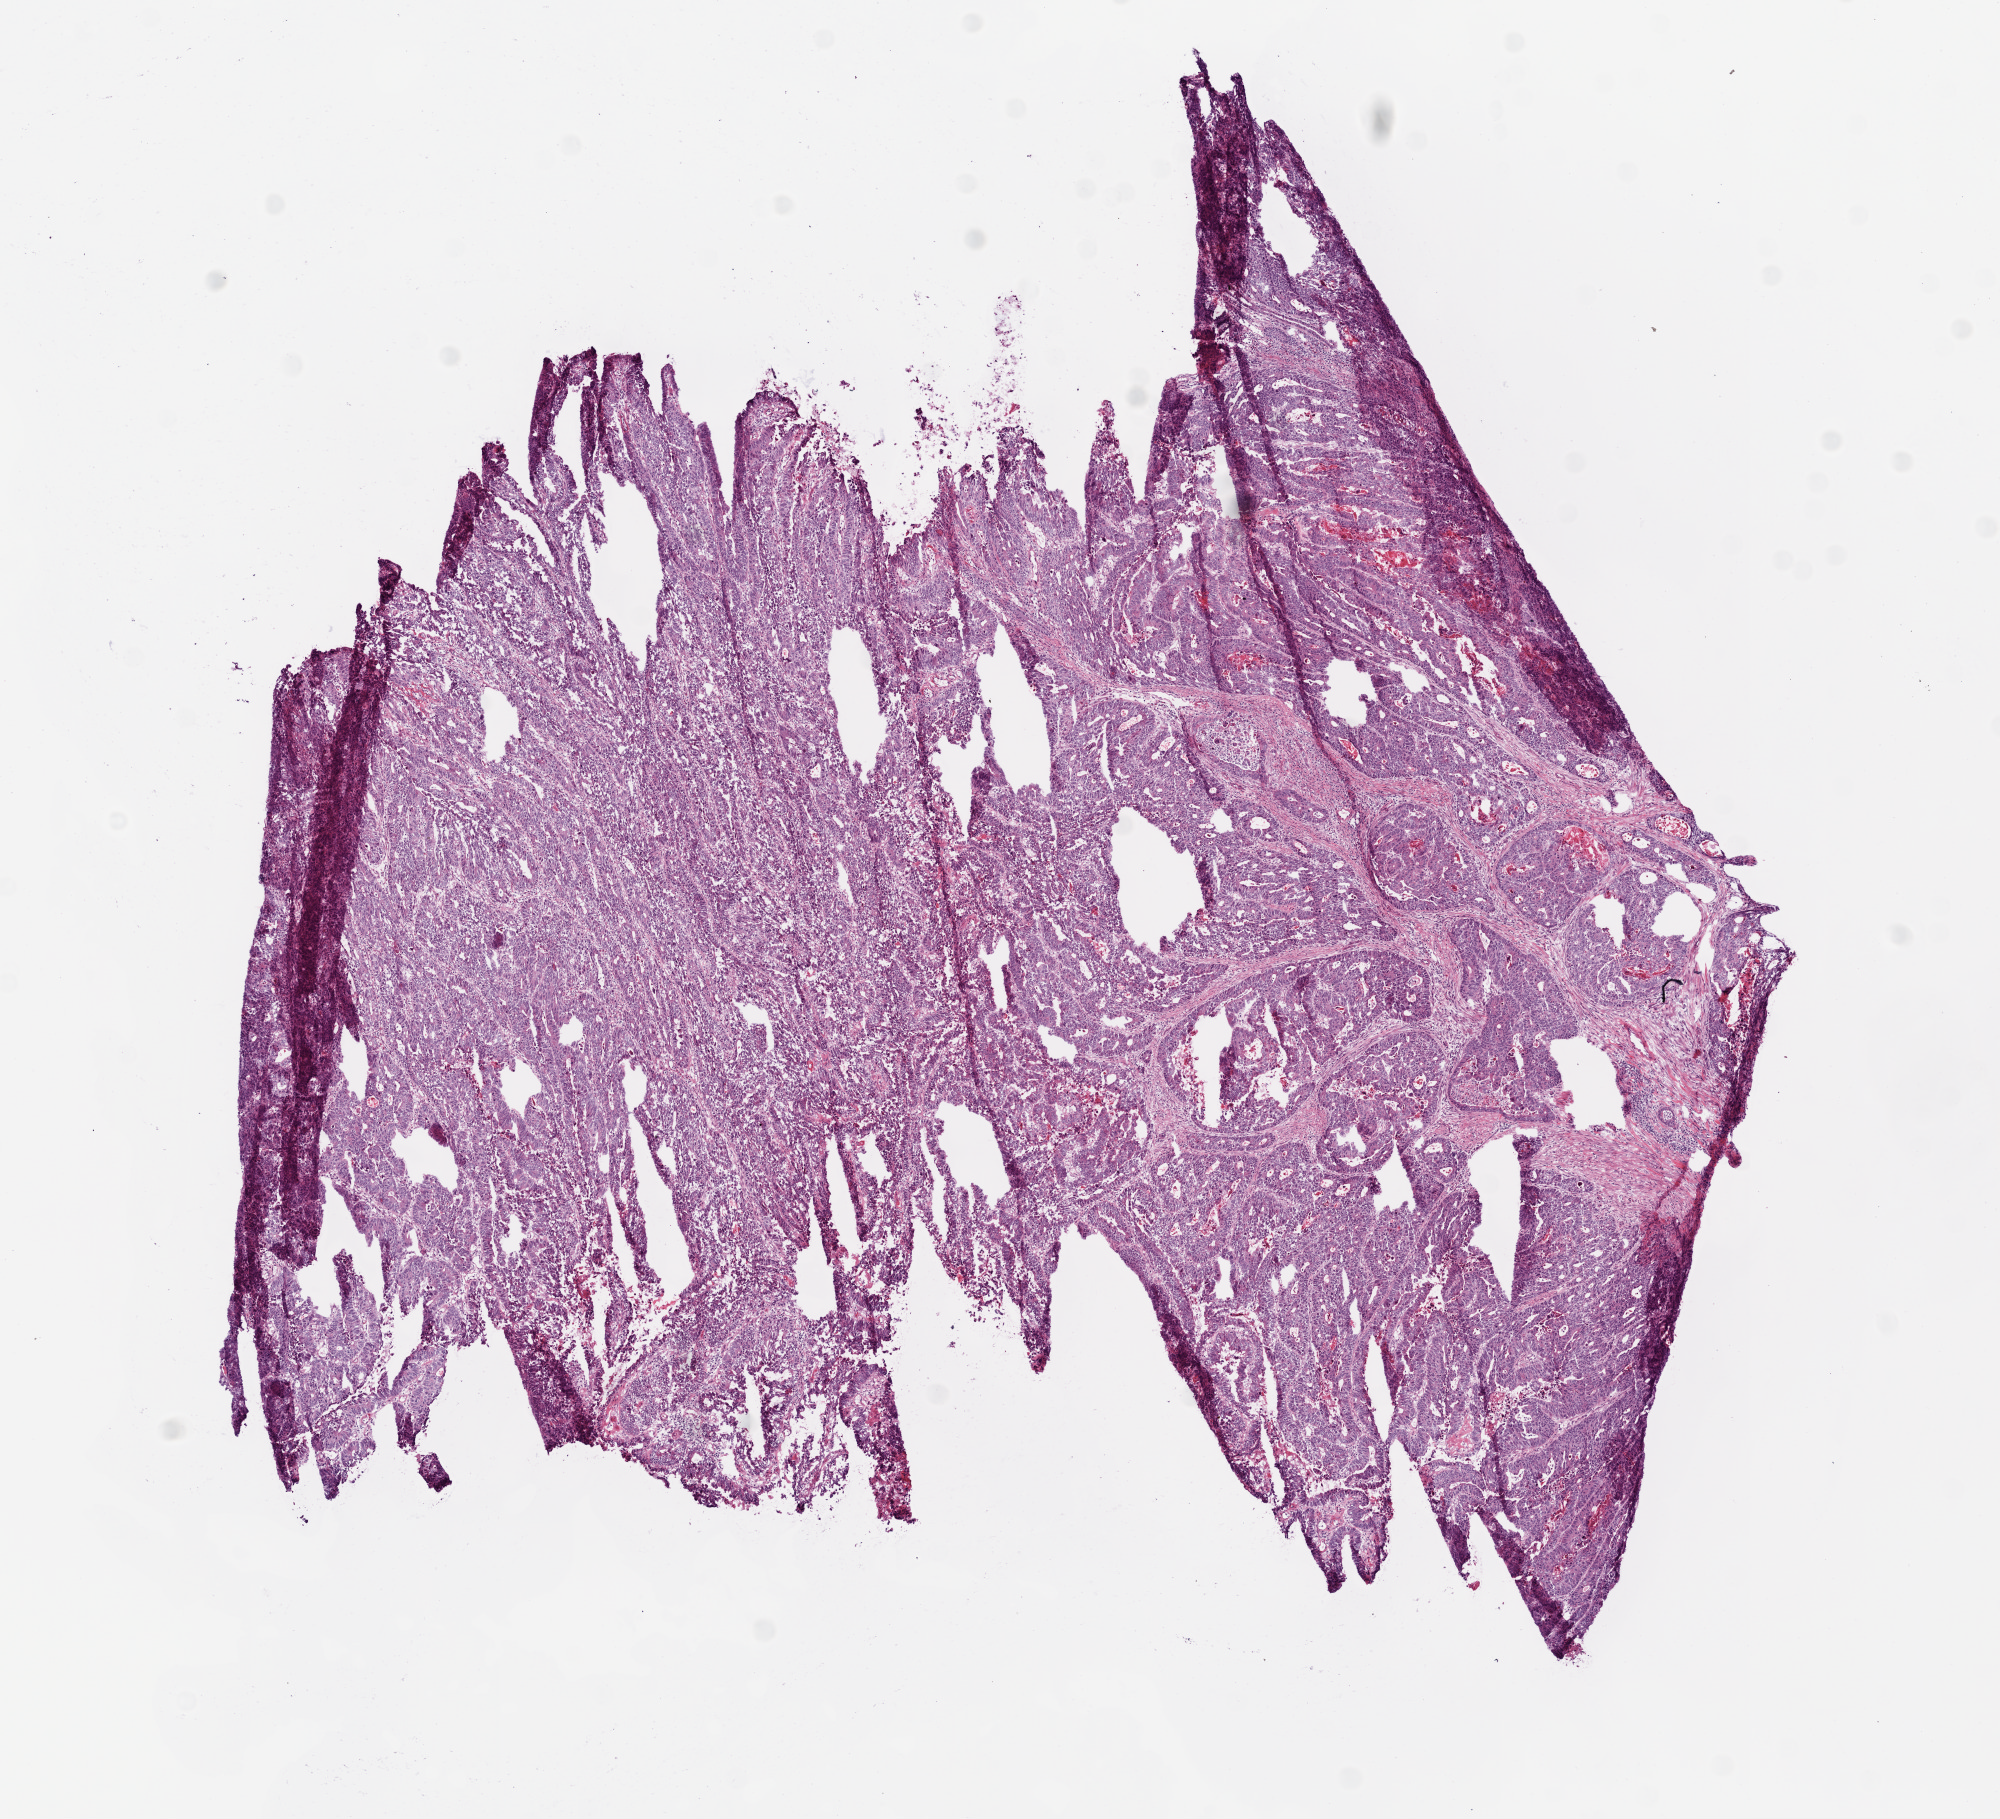
H&E whole-slide image — a low-resolution overview of the entire scanned area, about 8.0 x 7.3 mm (slide scanned at 20x), frozen section from the top of the tissue portion, primary tumour sample from the colon. Patient: male, age at initial diagnosis 60 years. Pathologist review of this section (percent, as recorded): tumour cells 90%, tumour nuclei 95%, normal cells 0%, stromal cells 10%, necrosis 0%.
AJCC pathologic stage: IIA. Diagnosis: Adenocarcinoma, NOS. Lymph nodes positive (case pathology): 0 of 54 examined. TNM: T3 N0 M0.